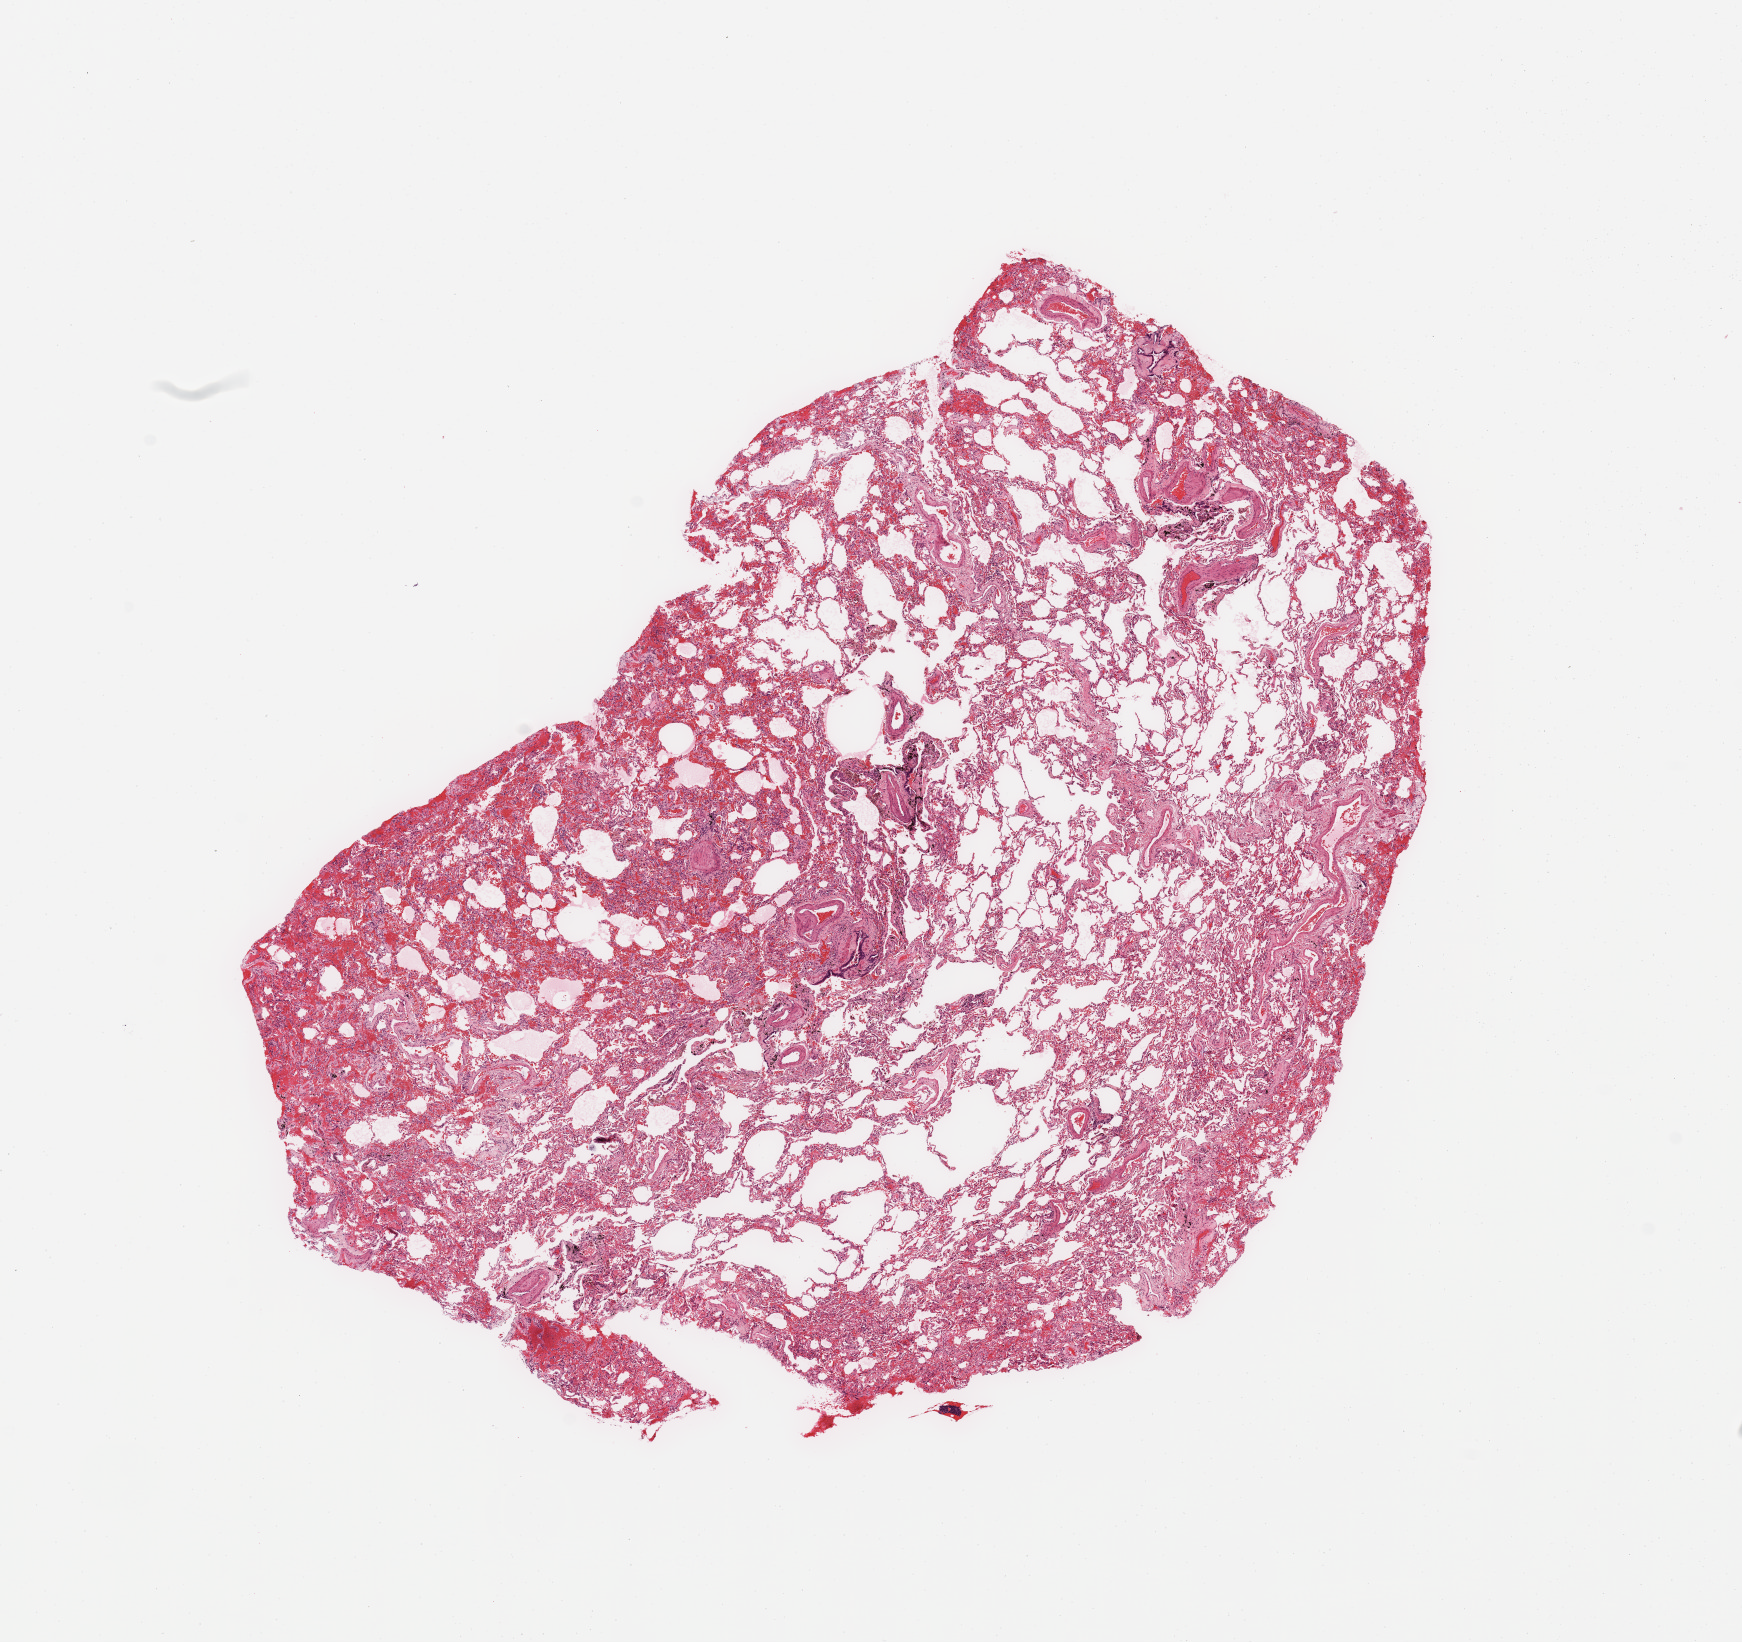
Digitized H&E-stained tissue section (whole slide), low-resolution overview of the scanned area, about 13.8 x 13.0 mm. Normal (non-tumour) tissue sample, sampled site: lung. Patient: male, age 54 years.
• this section: normal (non-tumour) tissue from the same patient
• patient diagnosis: Squamous cell carcinoma, NOS